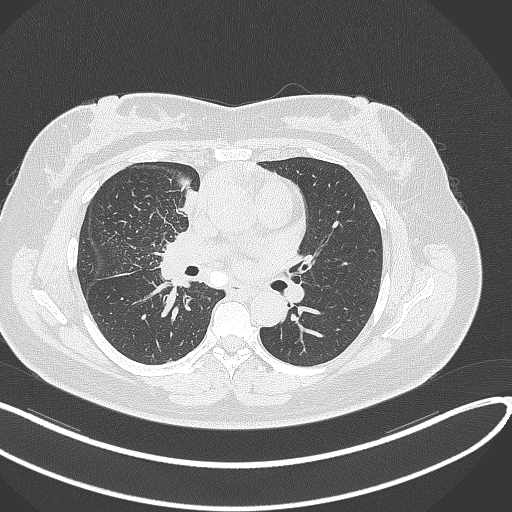
Chest CT, one axial slice; slice 143 of 303 in the series (ordered by position); reconstruction kernel B70f; 120 kVp; lung window (W 1500 / L -600 HU); 512 × 512 image matrix. Patient: female, 46 years. Case-level facts recorded for this patient, not image findings: clinical TNM (as recorded): T2a N1 M0.
Structures marked on this image (rectangle marked by the reading radiologist):
- lung tumour (recorded histology: adenocarcinoma): box from (x=174, y=186) to (x=201, y=221) px